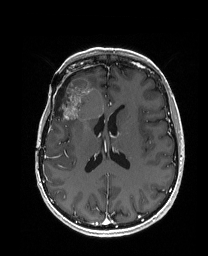
Brain MRI from a brain-tumour surgery series, one axial slice. Position 81 of 192 along the scan axis. T1-weighted post-contrast. 1 mm slice thickness. 208 × 256 image matrix, field of view 203 × 250 mm. Case-level facts recorded for this patient, not image findings: histopathology: Metastatic Carcinoma from Breast primary; tumour location: Right Frontal.
Outlined on this slice (manually delineated by an expert):
- previous resection cavity: bounding box [x1, y1, x2, y2] px = [54, 77, 71, 116]
- tumour: [55, 77, 104, 120]